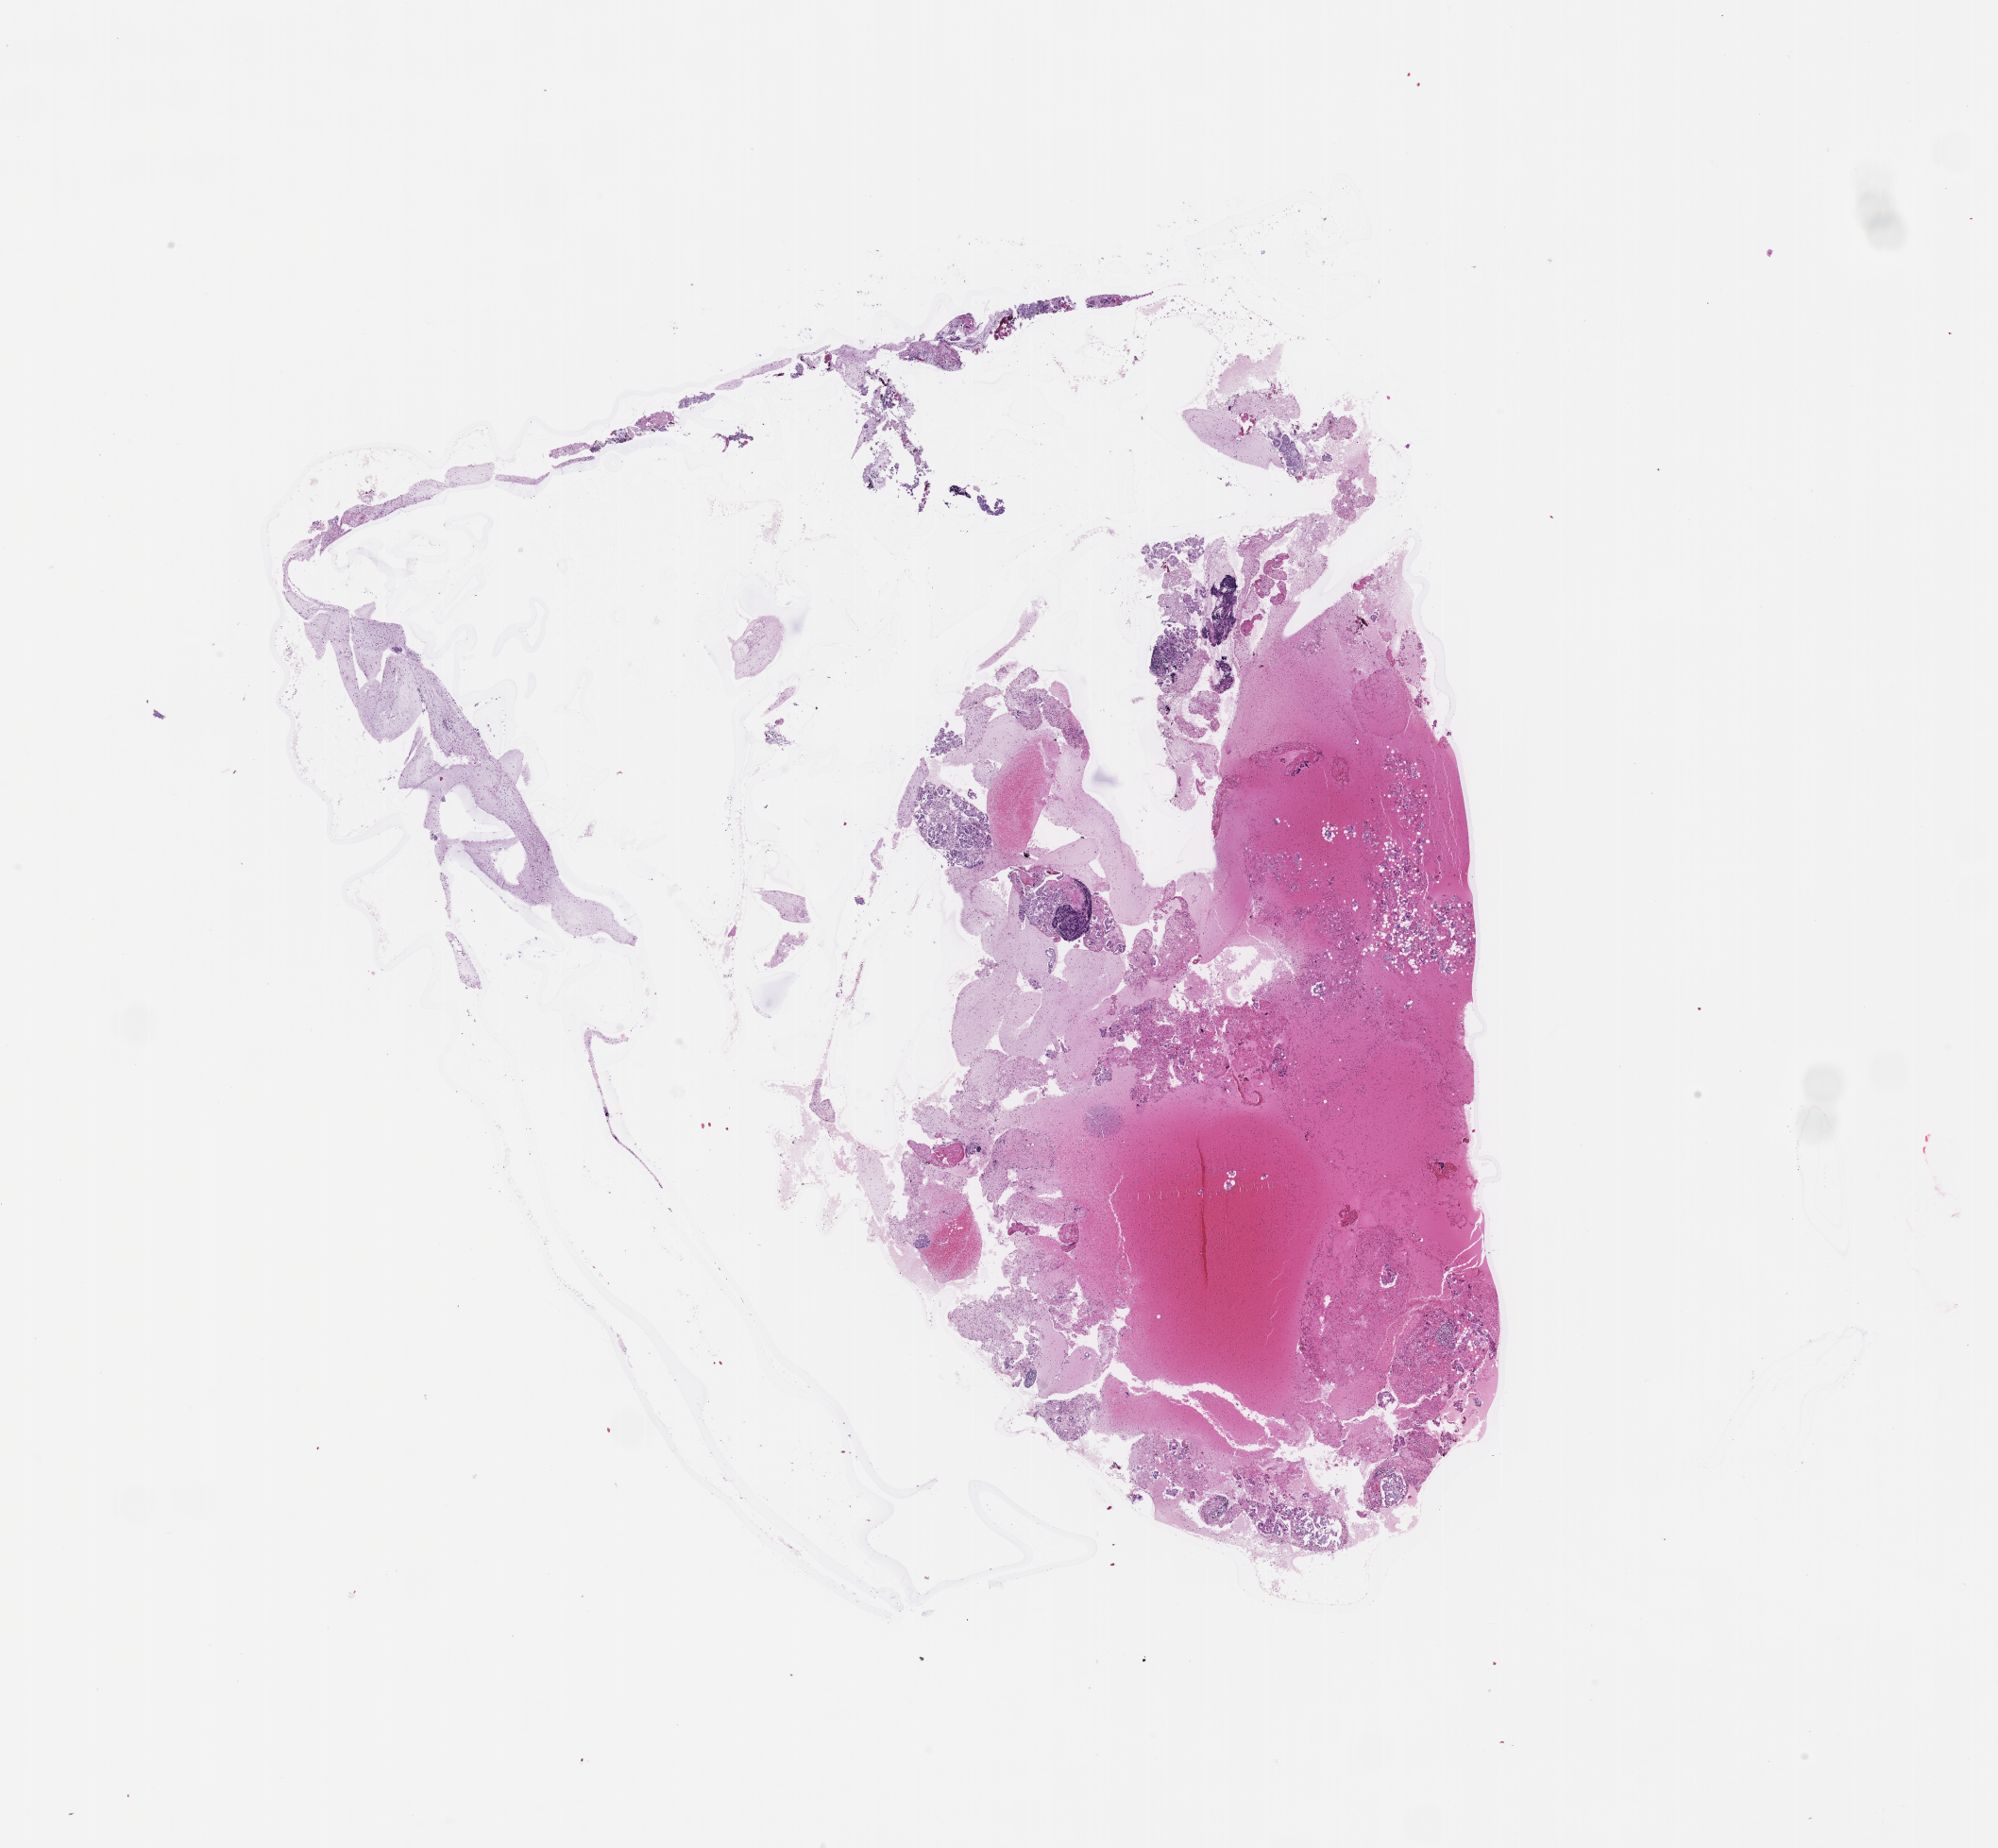
Haematoxylin and eosin whole-slide image, low-resolution overview of the scanned area, about 17.1 x 15.8 mm; FFPE section. Patient sex: male.
This section: metastatic tumor tissue. Patient diagnosis (primary): Non-Small Cell Lung Carcinoma.